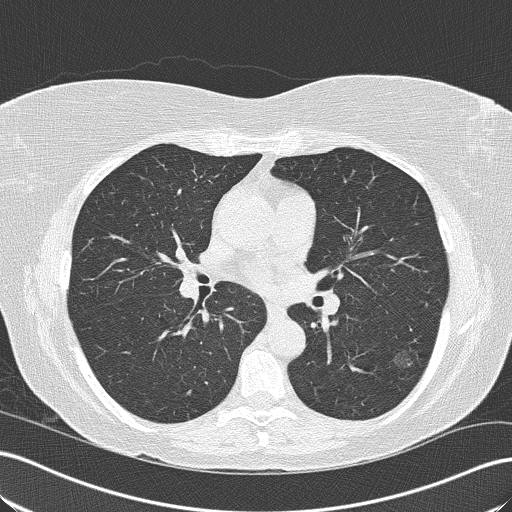
Low-dose screening chest CT, axial slice, second screening round (one year after baseline), lung window (W 1500 / L -600 HU), lung (sharp) reconstruction kernel (B50f), slice 84 of 165 in the series. Female, age 57 years at enrolment. Current smoker at enrolment.
Lesion marked by an expert reader, bounding box (x1, y1, x2, y2) in pixels: (379, 339, 429, 385). The screening reader recorded 6 non-calcified nodules or masses ≥4 mm on this exam (left lower lobe, right upper lobe, right upper lobe, right upper lobe, right lower lobe, right upper lobe); which of them this box marks is not recorded. Participant outcome: lung cancer diagnosed 482 days after this screen — bronchiolo-alveolar adenocarcinoma, NOS, left lower lobe, well differentiated (G1), stage IA (AJCC 6th edition), 16 mm at pathology.